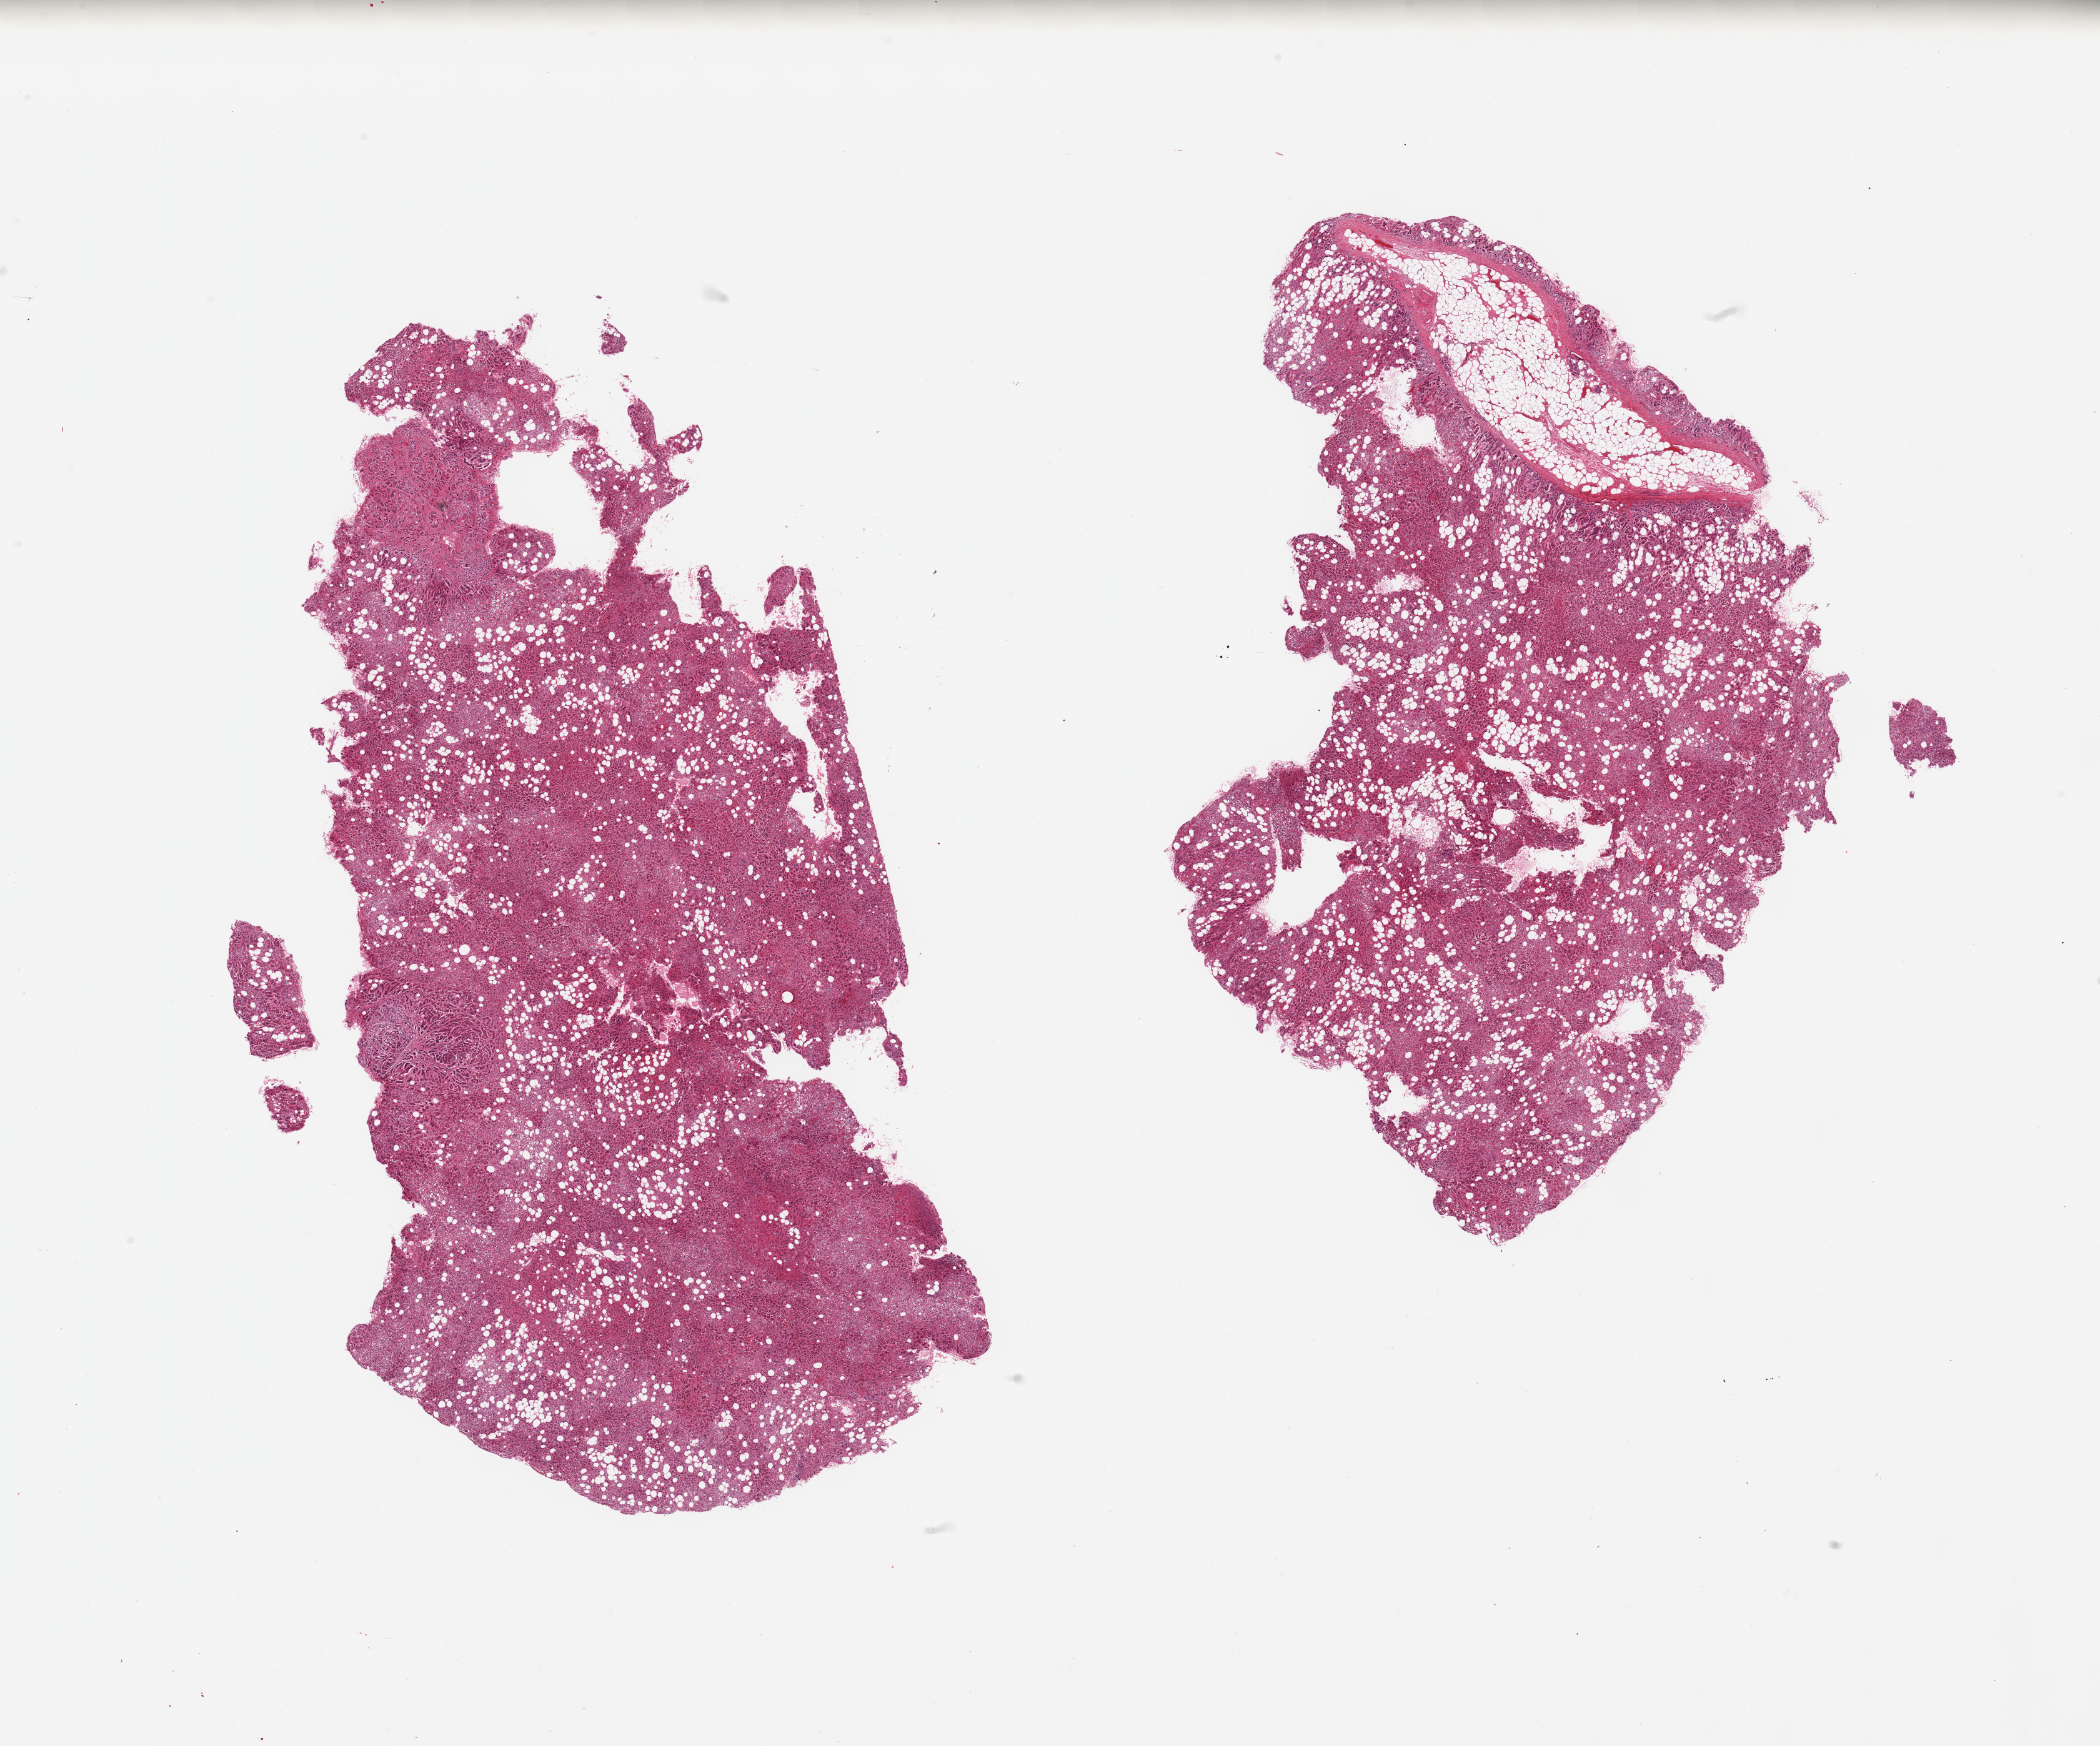
Hematoxylin and eosin (H&E) whole-slide image, a low-resolution overview of the entire scanned area, about 26.6 x 22.1 mm; PAXgene-fixed paraffin-embedded (PFPE) section; sampled site (target tissue): adrenal gland; tissue donor sample.
Review note (as recorded): 2 pieces; moderate to severe autolysis; diffuse dissemination of fat droplets (fatty degeneration); ~20% focal internal fat; focal stromal fibrosis; congestion.